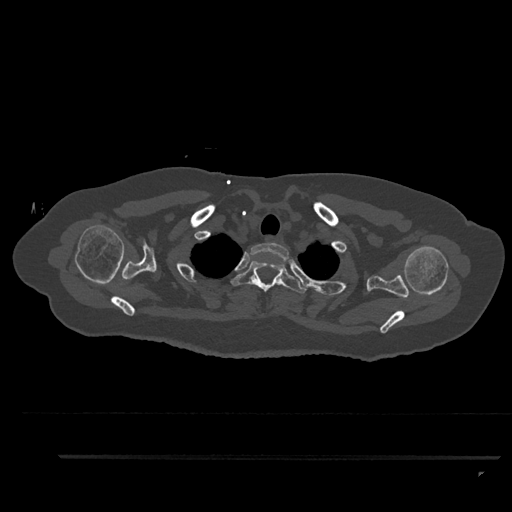
CT including the spine, one axial slice; position 734 of 797 along the scan axis; reconstruction kernel Br40s/3; 120 kVp; bone window (W 1800 / L 400 HU); 0.5 mm slice thickness; 512 × 512 image matrix, field of view 408 × 408 mm. Female patient, age 44 years. Case-level facts recorded for this patient, not image findings: primary cancer: renal.
Outlined on this slice (semi-automatically segmented with operator editing):
- T1 vertebra: box from (x=249, y=243) to (x=289, y=263) px
- T2 vertebra: (x=230, y=260)–(x=307, y=293)